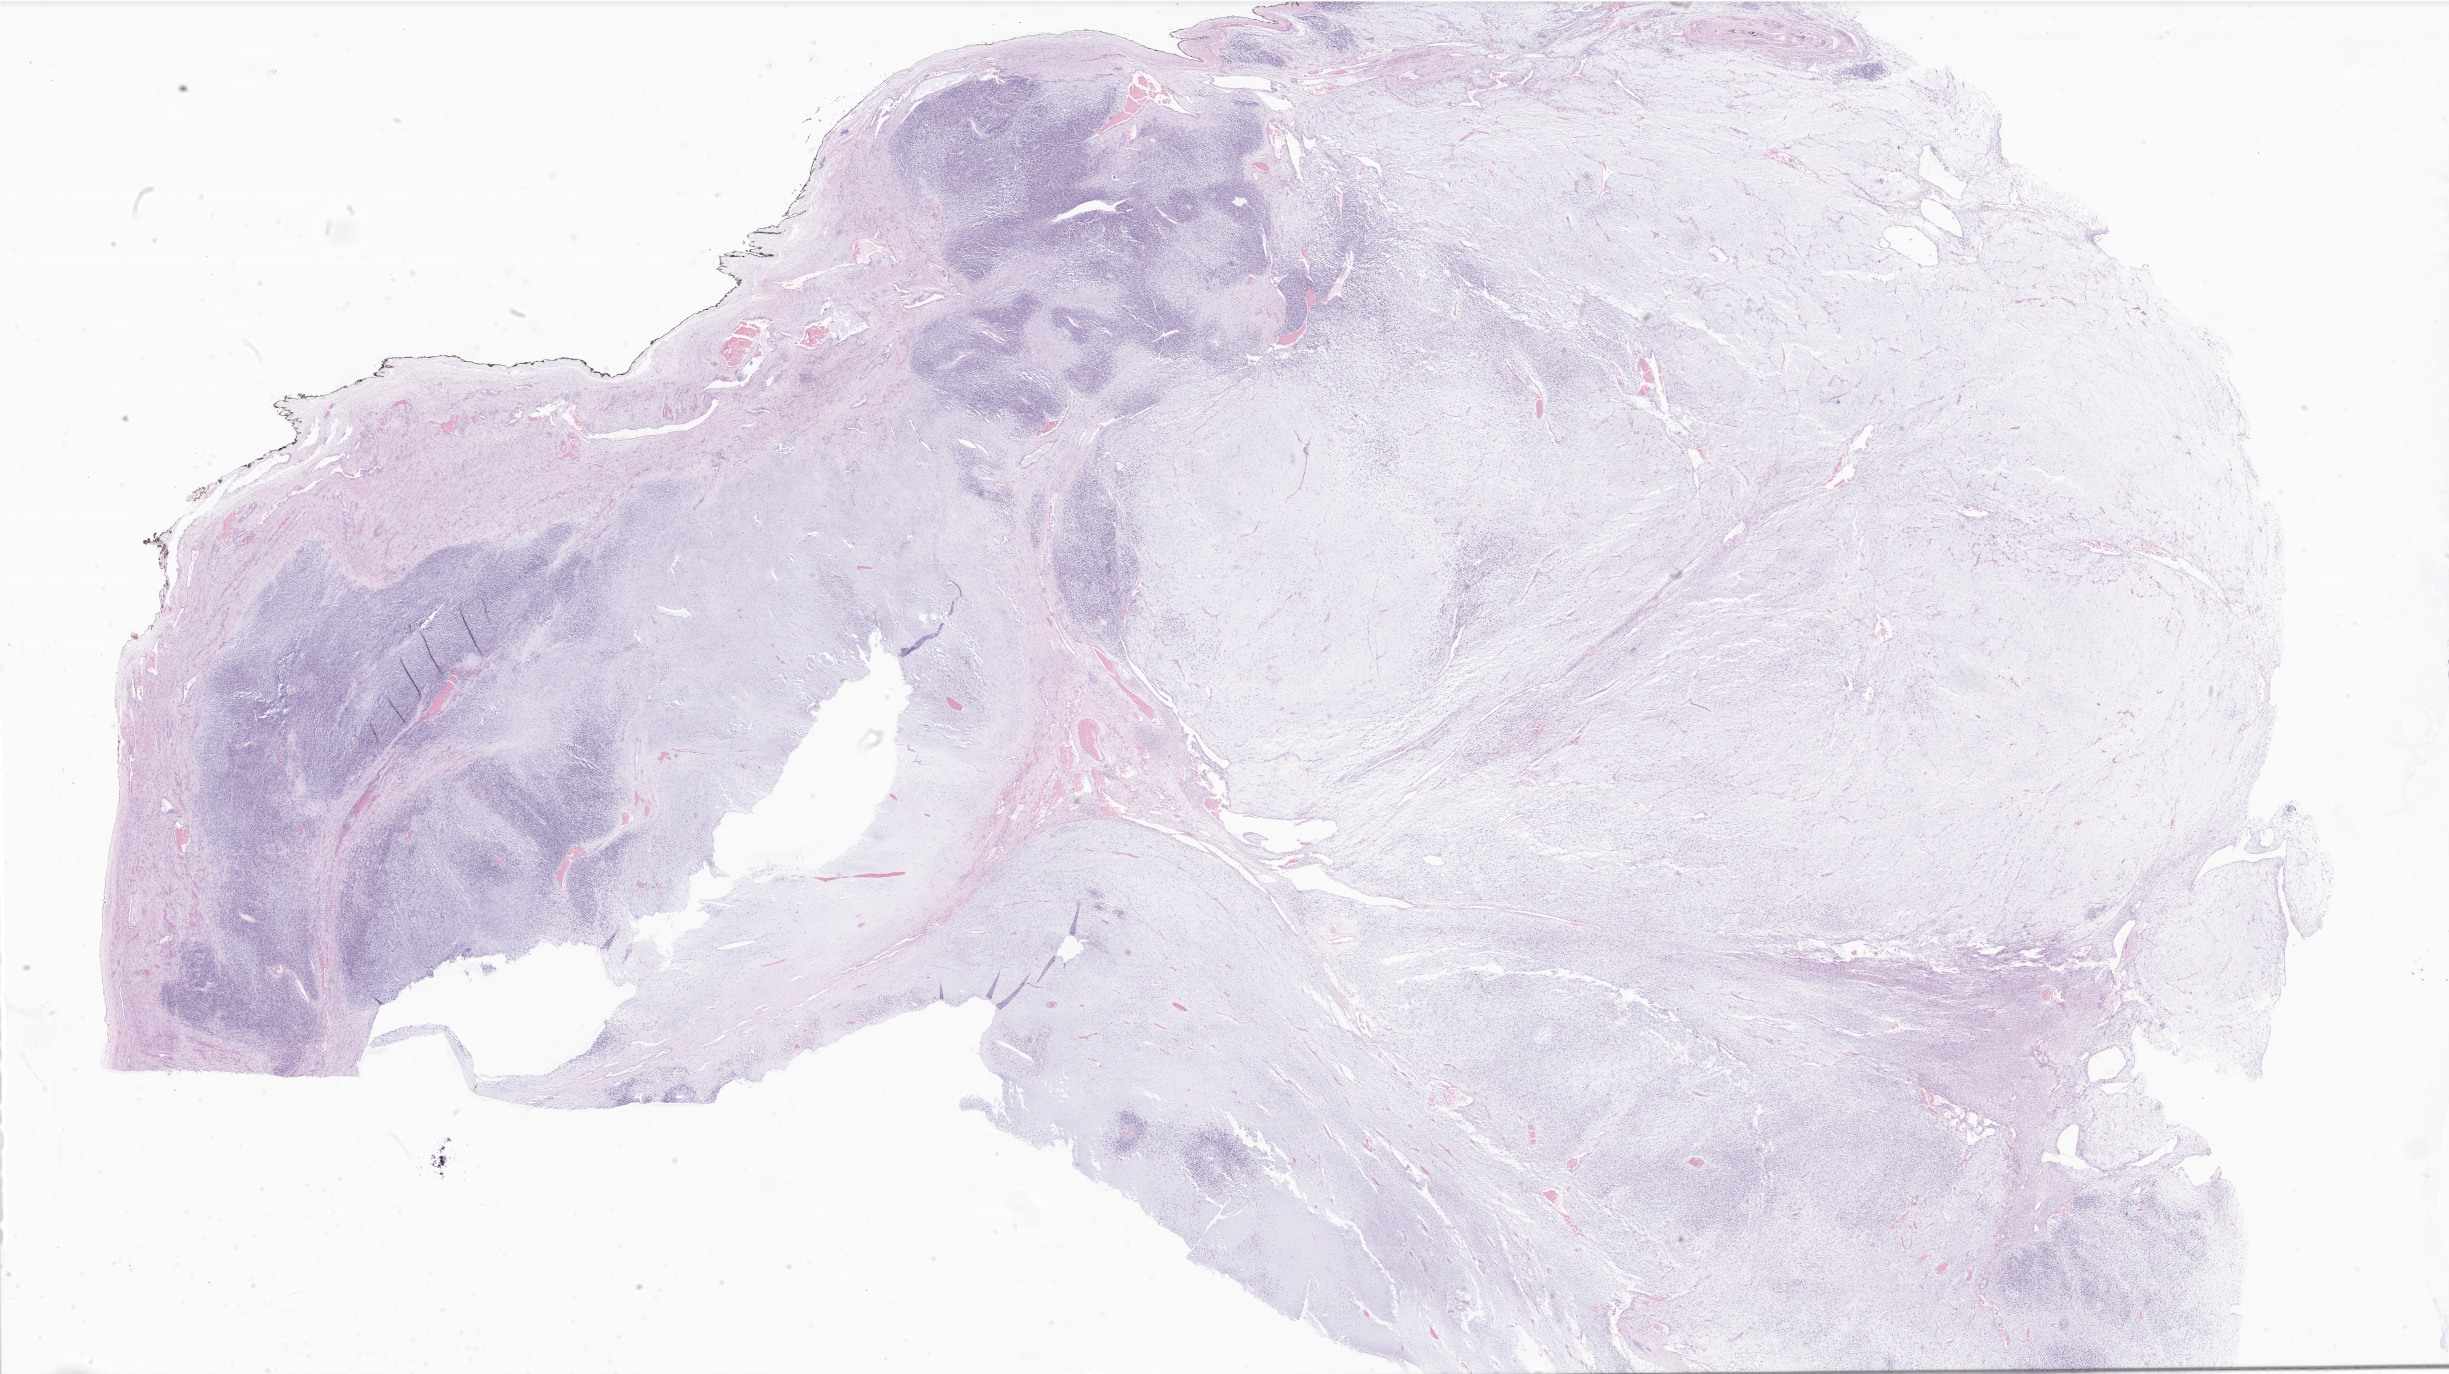
Whole-slide image, haematoxylin and eosin stain of tumor tissue from the testis — shown as a low-resolution overview of the whole scanned area (about 41.3 x 23.2 mm); formalin-fixed, paraffin-embedded (FFPE) tissue. Patient male; age 41 months (3 years 5 months).
Diagnosis (ICD-O-3 morphology term): Embryonal rhabdomyosarcoma, NOS.